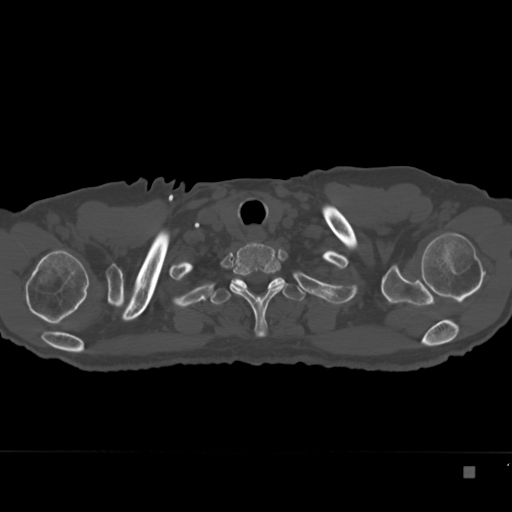
CT including the spine, one axial slice. Reconstruction kernel Br40s. 120 kVp. Bone window (W 1800 / L 400 HU). 1.5 mm slice thickness. 512 × 512 image matrix. Patient: male, 72 years. From the clinical record (not read from this slice): primary cancer: skeletal.
Structures marked on this image (semi-automatic segmentation, software-assisted and operator-edited):
- T1 vertebra: bounding box <230,242,281,337> (left, top, right, bottom; pixels)
- T2 vertebra: <211,273,306,305>